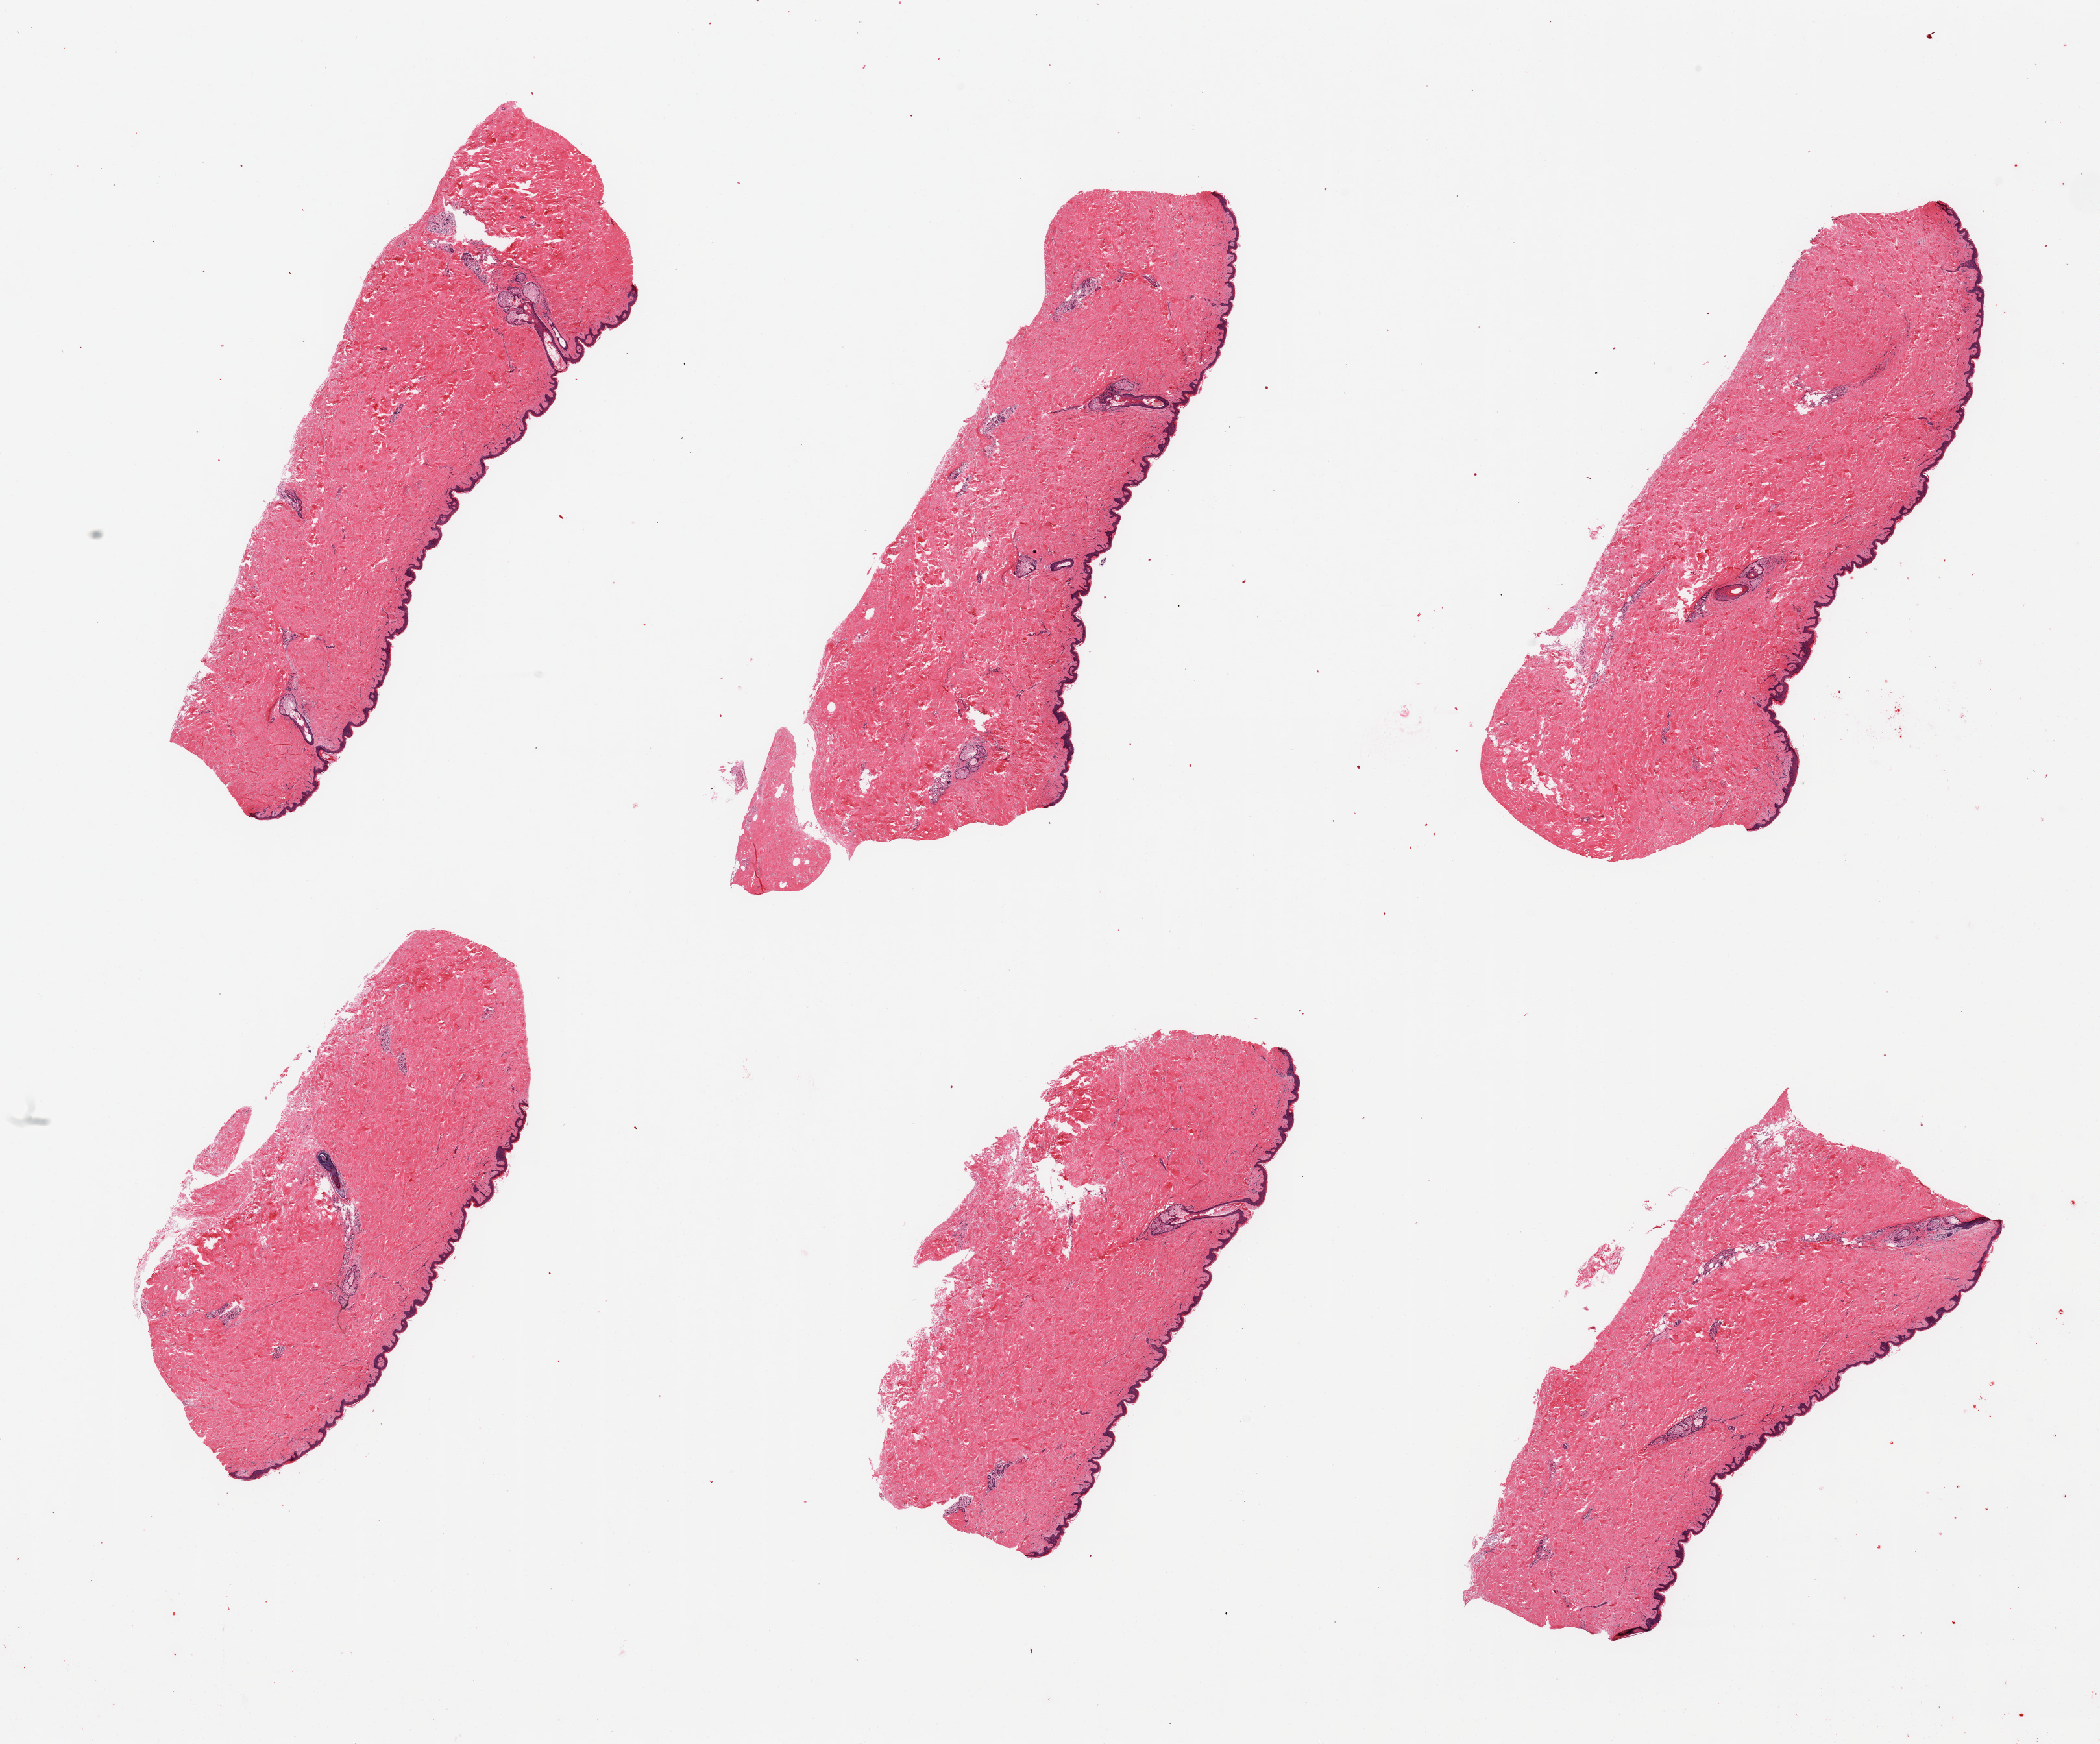
Digitized haematoxylin and eosin-stained section, a low-resolution overview of the entire scanned area, about 25.6 x 21.3 mm. PAXgene-fixed paraffin-embedded (PFPE) section. Target tissue: skin of suprapubic region. Donor tissue sample.
• review note (as recorded): 6 pieces, no significant dermal fat; squamous epithelium is ~35-40 microns